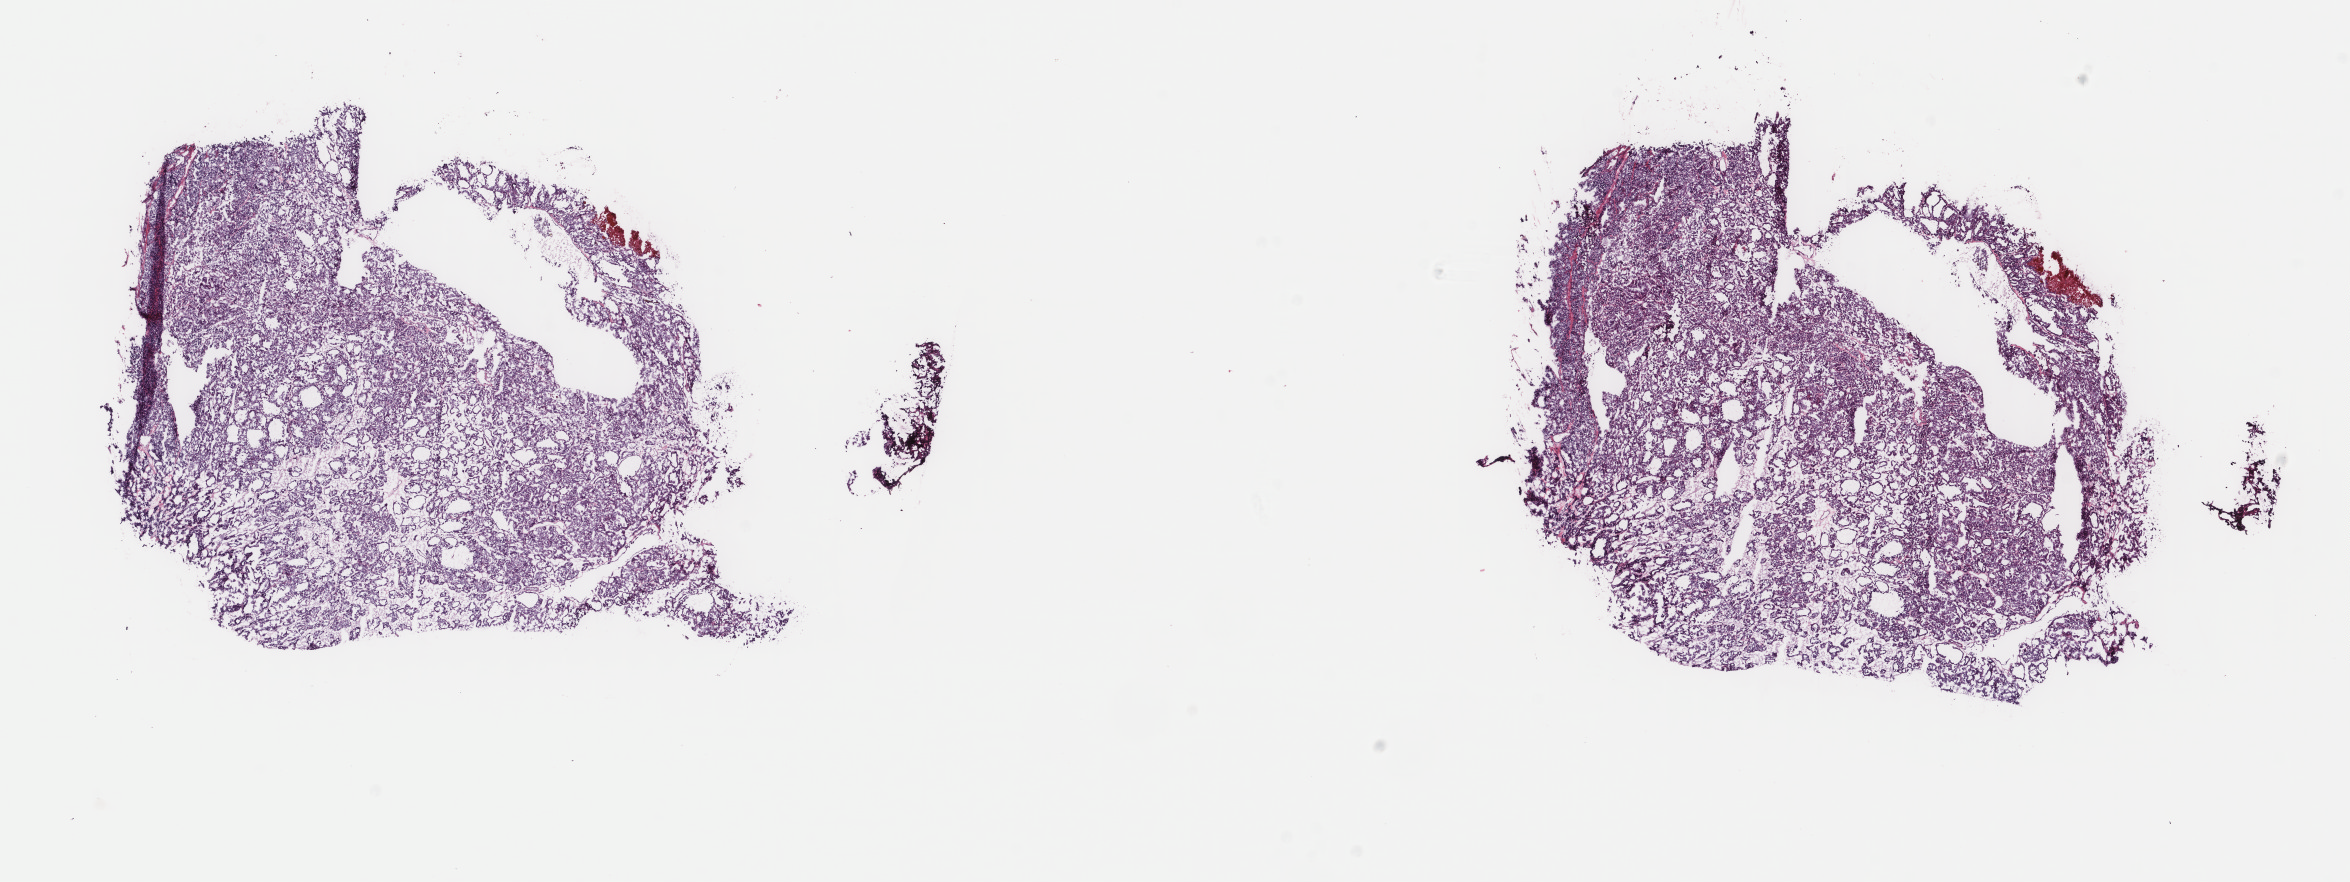
Digitized H&E tissue section (whole slide) — low-resolution overview of the scanned area, about 18.7 x 7.0 mm (acquisition: 40x scan), frozen section from the top of the tissue portion, sample: primary tumour, thyroid. Female, age 53 years at initial diagnosis. Composition of this section per pathologist review: tumour cells 90%, tumour nuclei 100%, normal cells 0%, stromal cells 10%, necrosis 0%. Infiltration values recorded for this section: lymphocyte infiltration 0%, monocyte infiltration 0%, neutrophil infiltration 0%.
- lymph nodes positive (case pathology): 5 of 54 examined
- AJCC pathologic stage: IVA
- histologic diagnosis: Papillary carcinoma, follicular variant (thyroid gland)